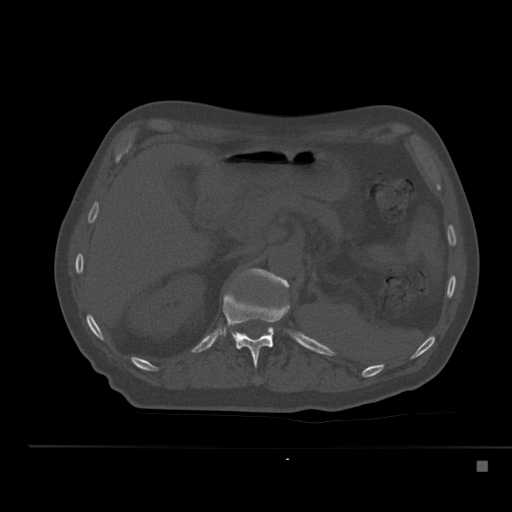
CT including the spine, one axial slice; position 225 of 517 along the scan axis; 120 kVp; bone window (W 1800 / L 400 HU); 1.5 mm slice thickness; 512 × 512 image matrix, field of view 408 × 408 mm. Patient: male, 70 years. Case-level facts recorded for this patient, not image findings: primary cancer: renal; vertebrae with lytic lesions (as recorded): T4, T6, T10, T12, L3, L4, L5.
Annotated regions visible in this slice (semi-automatically segmented with operator editing):
- L1 vertebra: box from (x=251, y=268) to (x=289, y=333) px
- T12 vertebra: (x=223, y=290)–(x=290, y=368)